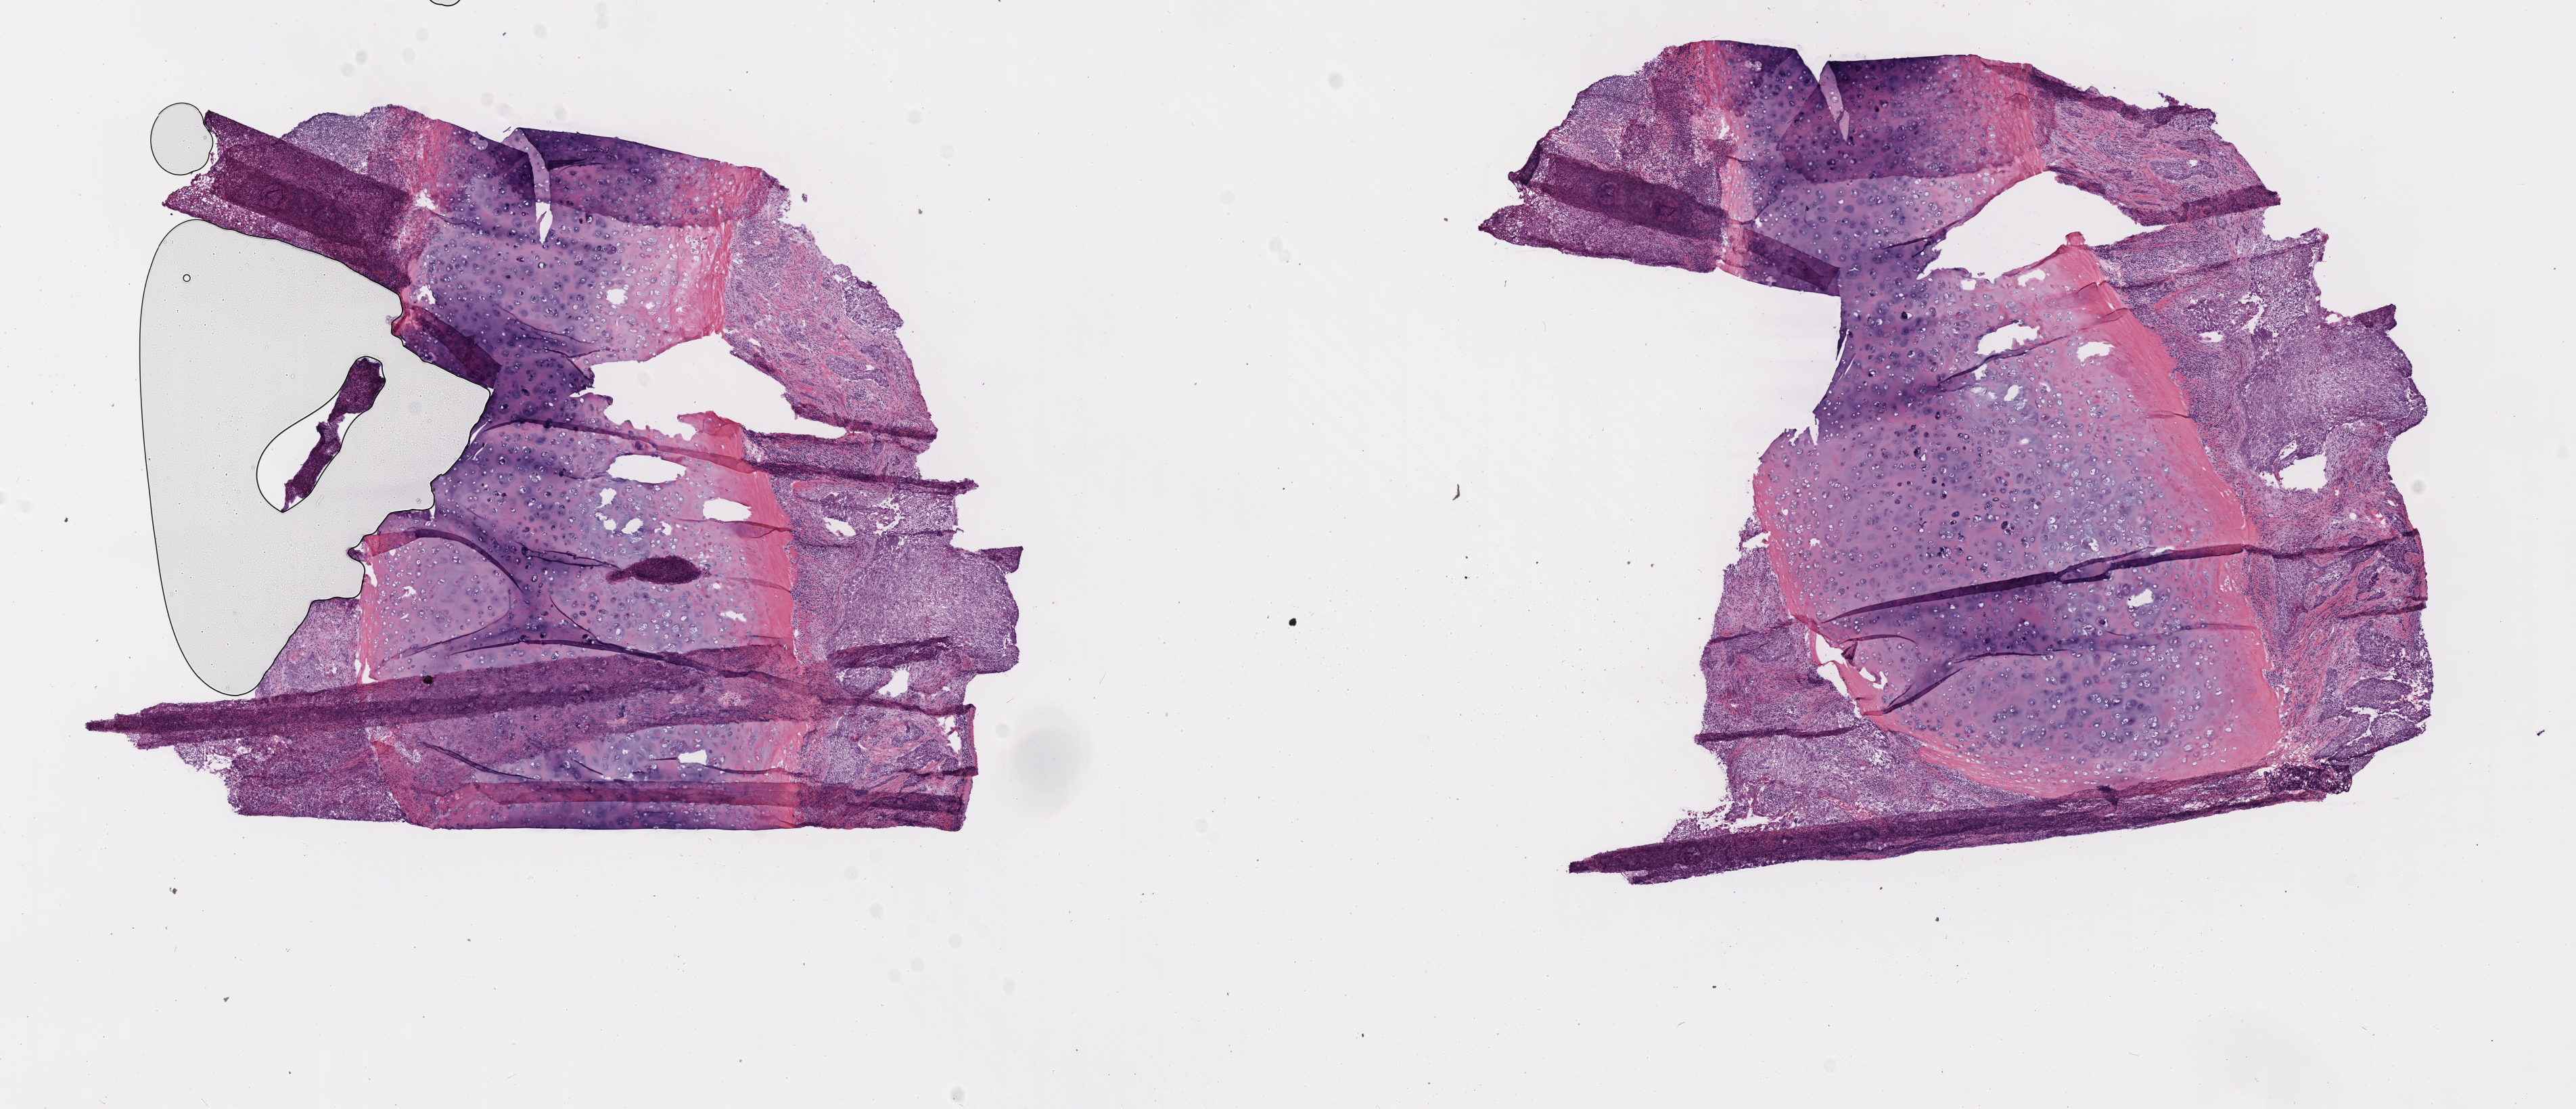
H&E whole-slide image, shown as a low-resolution overview of the whole scanned area (about 15.0 x 6.5 mm, slide scanned at 40x), frozen section from the bottom of the tissue portion, lung, primary tumour sample. Male patient; age at initial diagnosis 55 years. Composition of this section per pathologist review: tumour cells 40%, tumour nuclei 61%, normal cells 60%, stromal cells 0%, necrosis 0%. Inflammatory infiltration, as recorded: lymphocyte infiltration 20%, monocyte infiltration 0%, neutrophil infiltration 0%.
• pathologic diagnosis: Squamous cell carcinoma, NOS
• TNM: T2b N1 MX
• AJCC pathologic stage: IIB (7th edition)